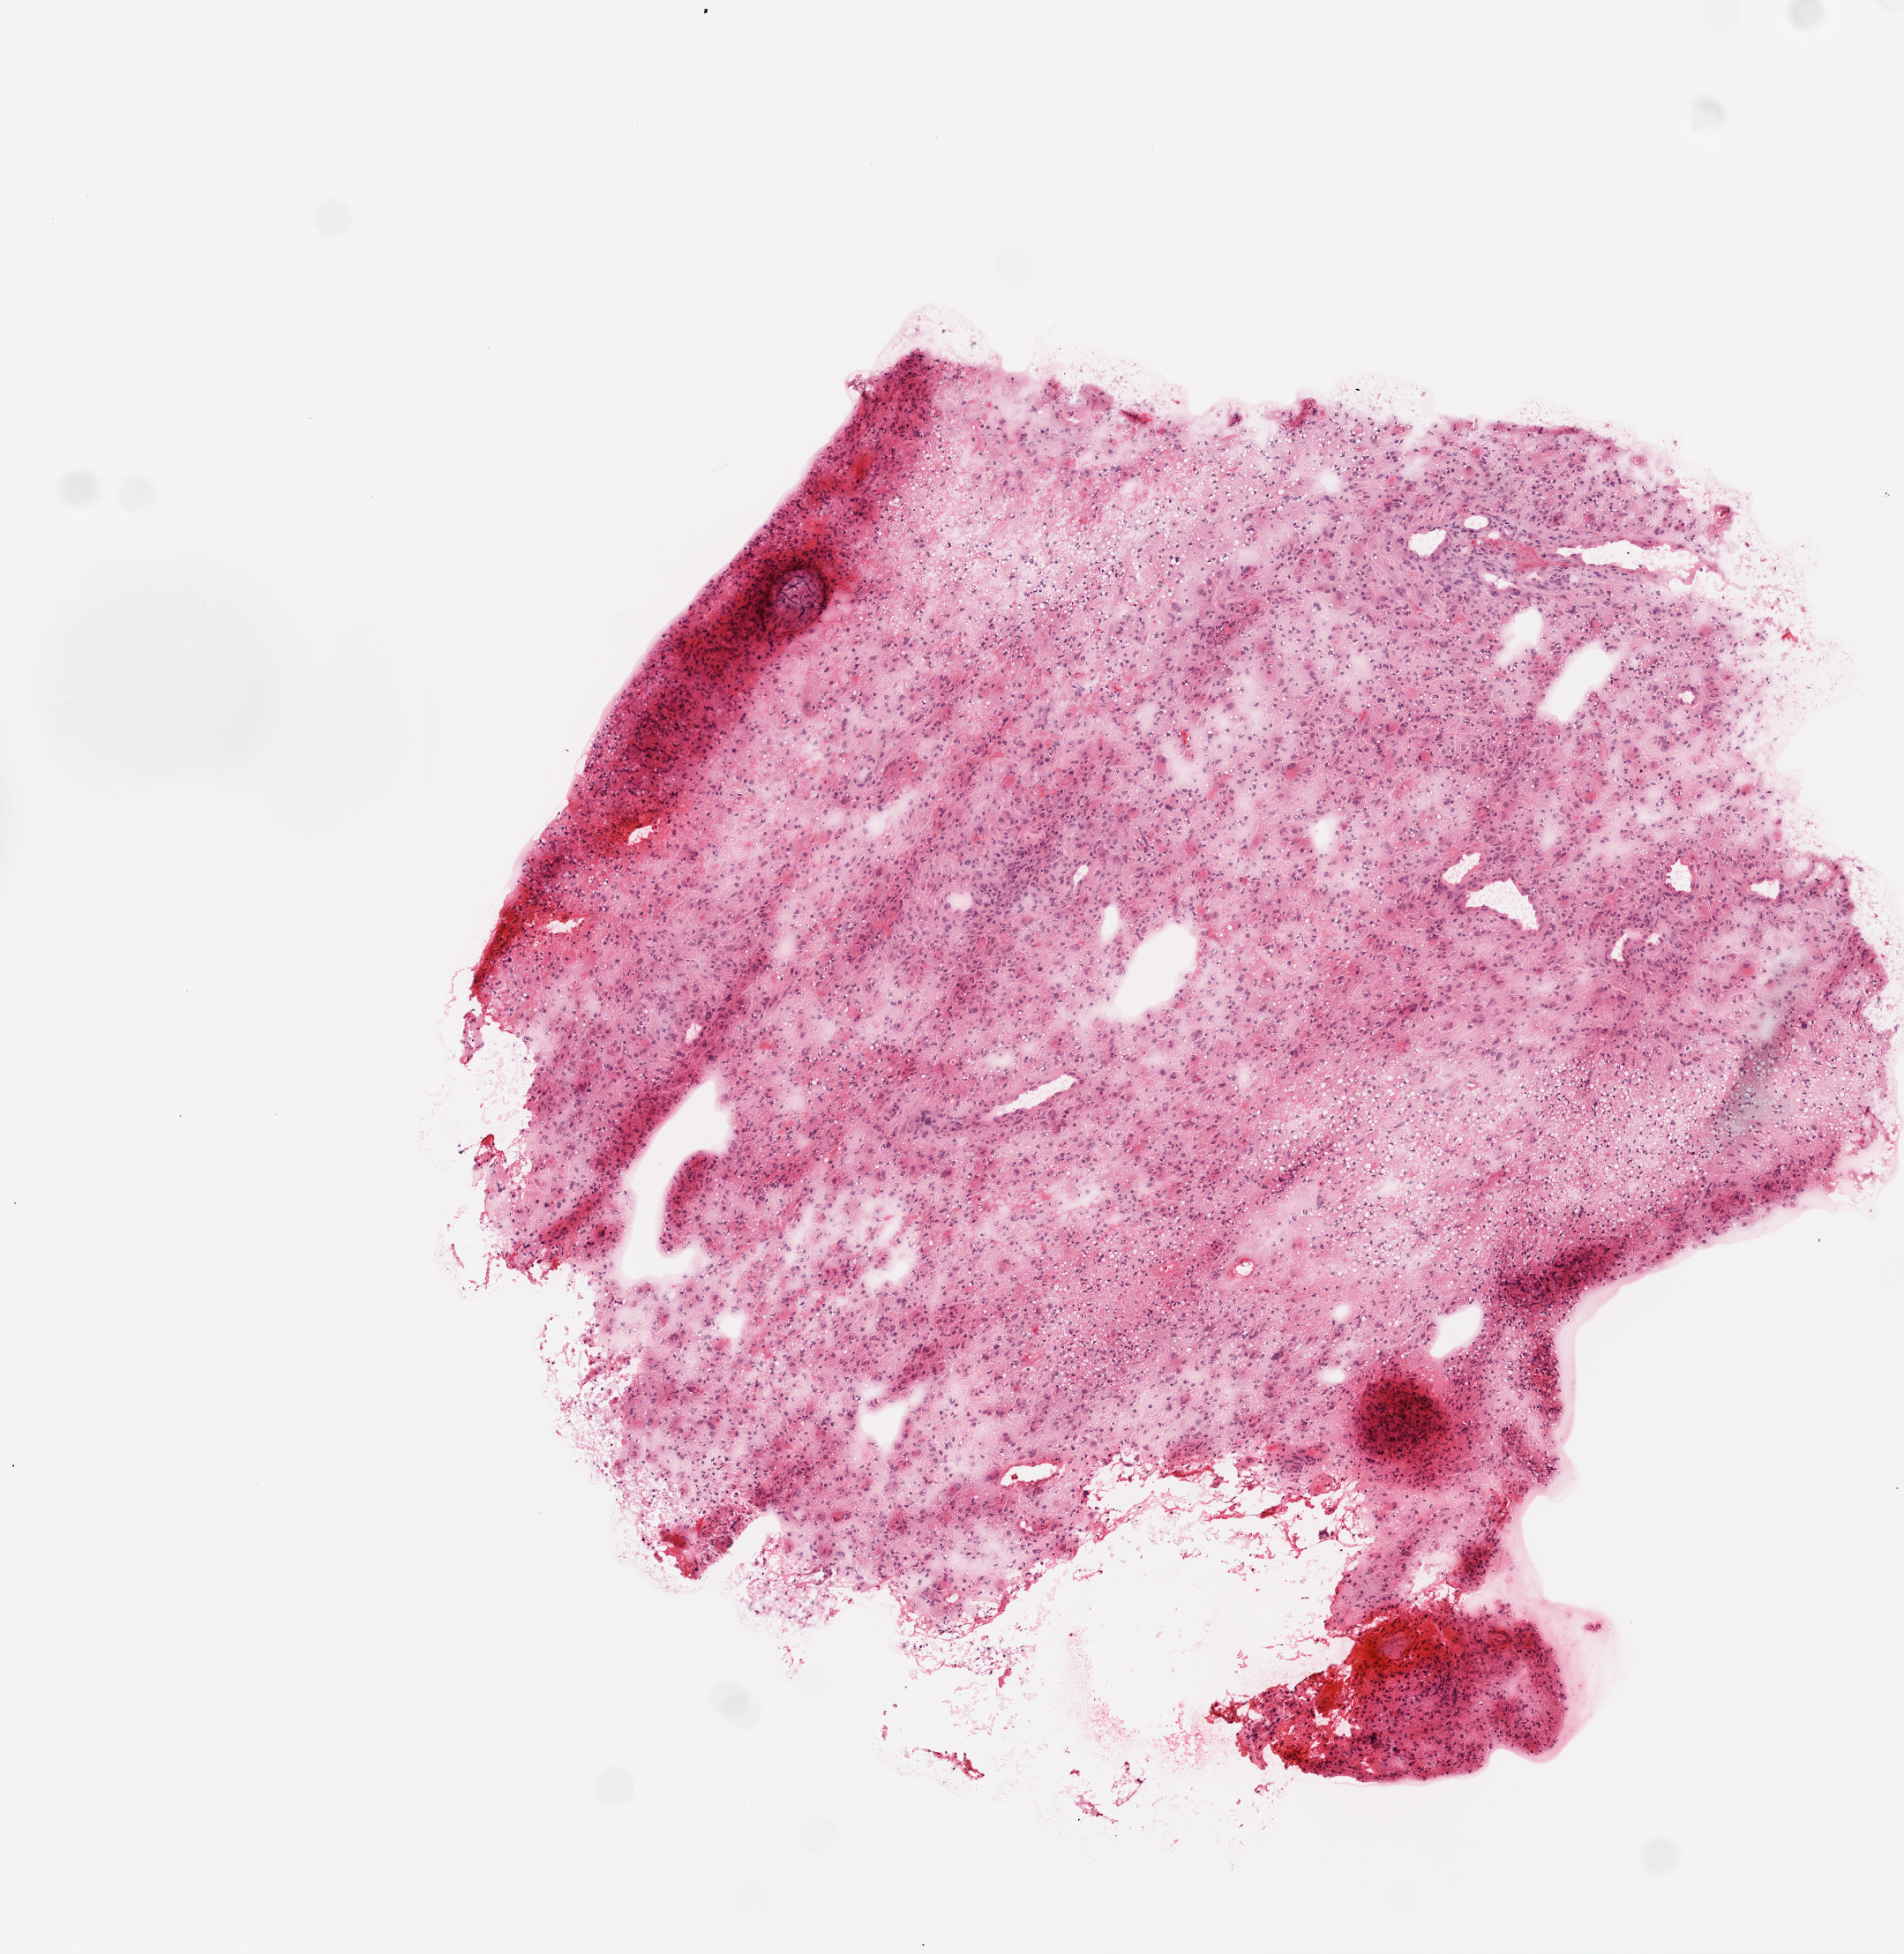
Whole-slide histology image, Hematoxylin and eosin (H&E) stained, low-resolution overview of the scanned area, about 4.4 x 4.5 mm, frozen section, primary tumour sample from the brain. Patient: male, age at initial diagnosis 76 years. Composition of this section per pathologist review: tumour cells 75%, tumour nuclei 85%, normal cells 0%, stromal cells 5%, necrosis 20%.
* histologic diagnosis: Glioblastoma